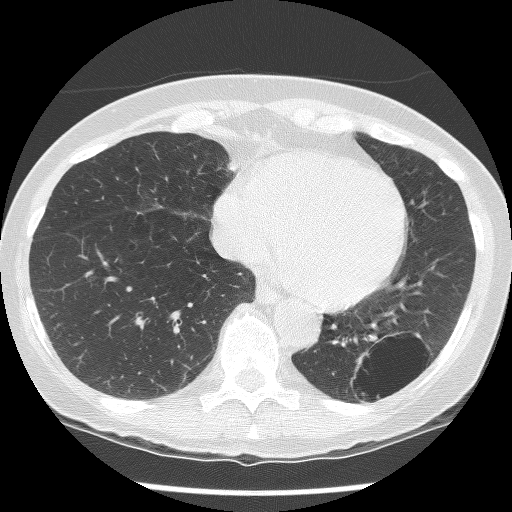
Low-dose screening chest CT, axial slice, second annual screen, lung window (W 1500 / L -600 HU), 2.5 mm slice thickness, lung (sharp) reconstruction kernel (BONE), 120 kVp. Female, age 61 years at enrolment. Current smoker at enrolment.
Lesion marked by an expert reader, box from (x=332, y=326) to (x=437, y=416) px. The screening reader recorded 2 non-calcified nodules or masses ≥4 mm on this exam (left lower lobe, left lower lobe); which of them this box marks is not recorded. Official screen result: positive, no significant change: stable abnormalities potentially related to lung cancer, unchanged since the prior screening exam. Later outcome: lung cancer diagnosed 585 days after this screen — non-small cell carcinoma, left lower lobe, poorly differentiated (G3), stage IB (AJCC 6th edition), 100 mm at pathology.